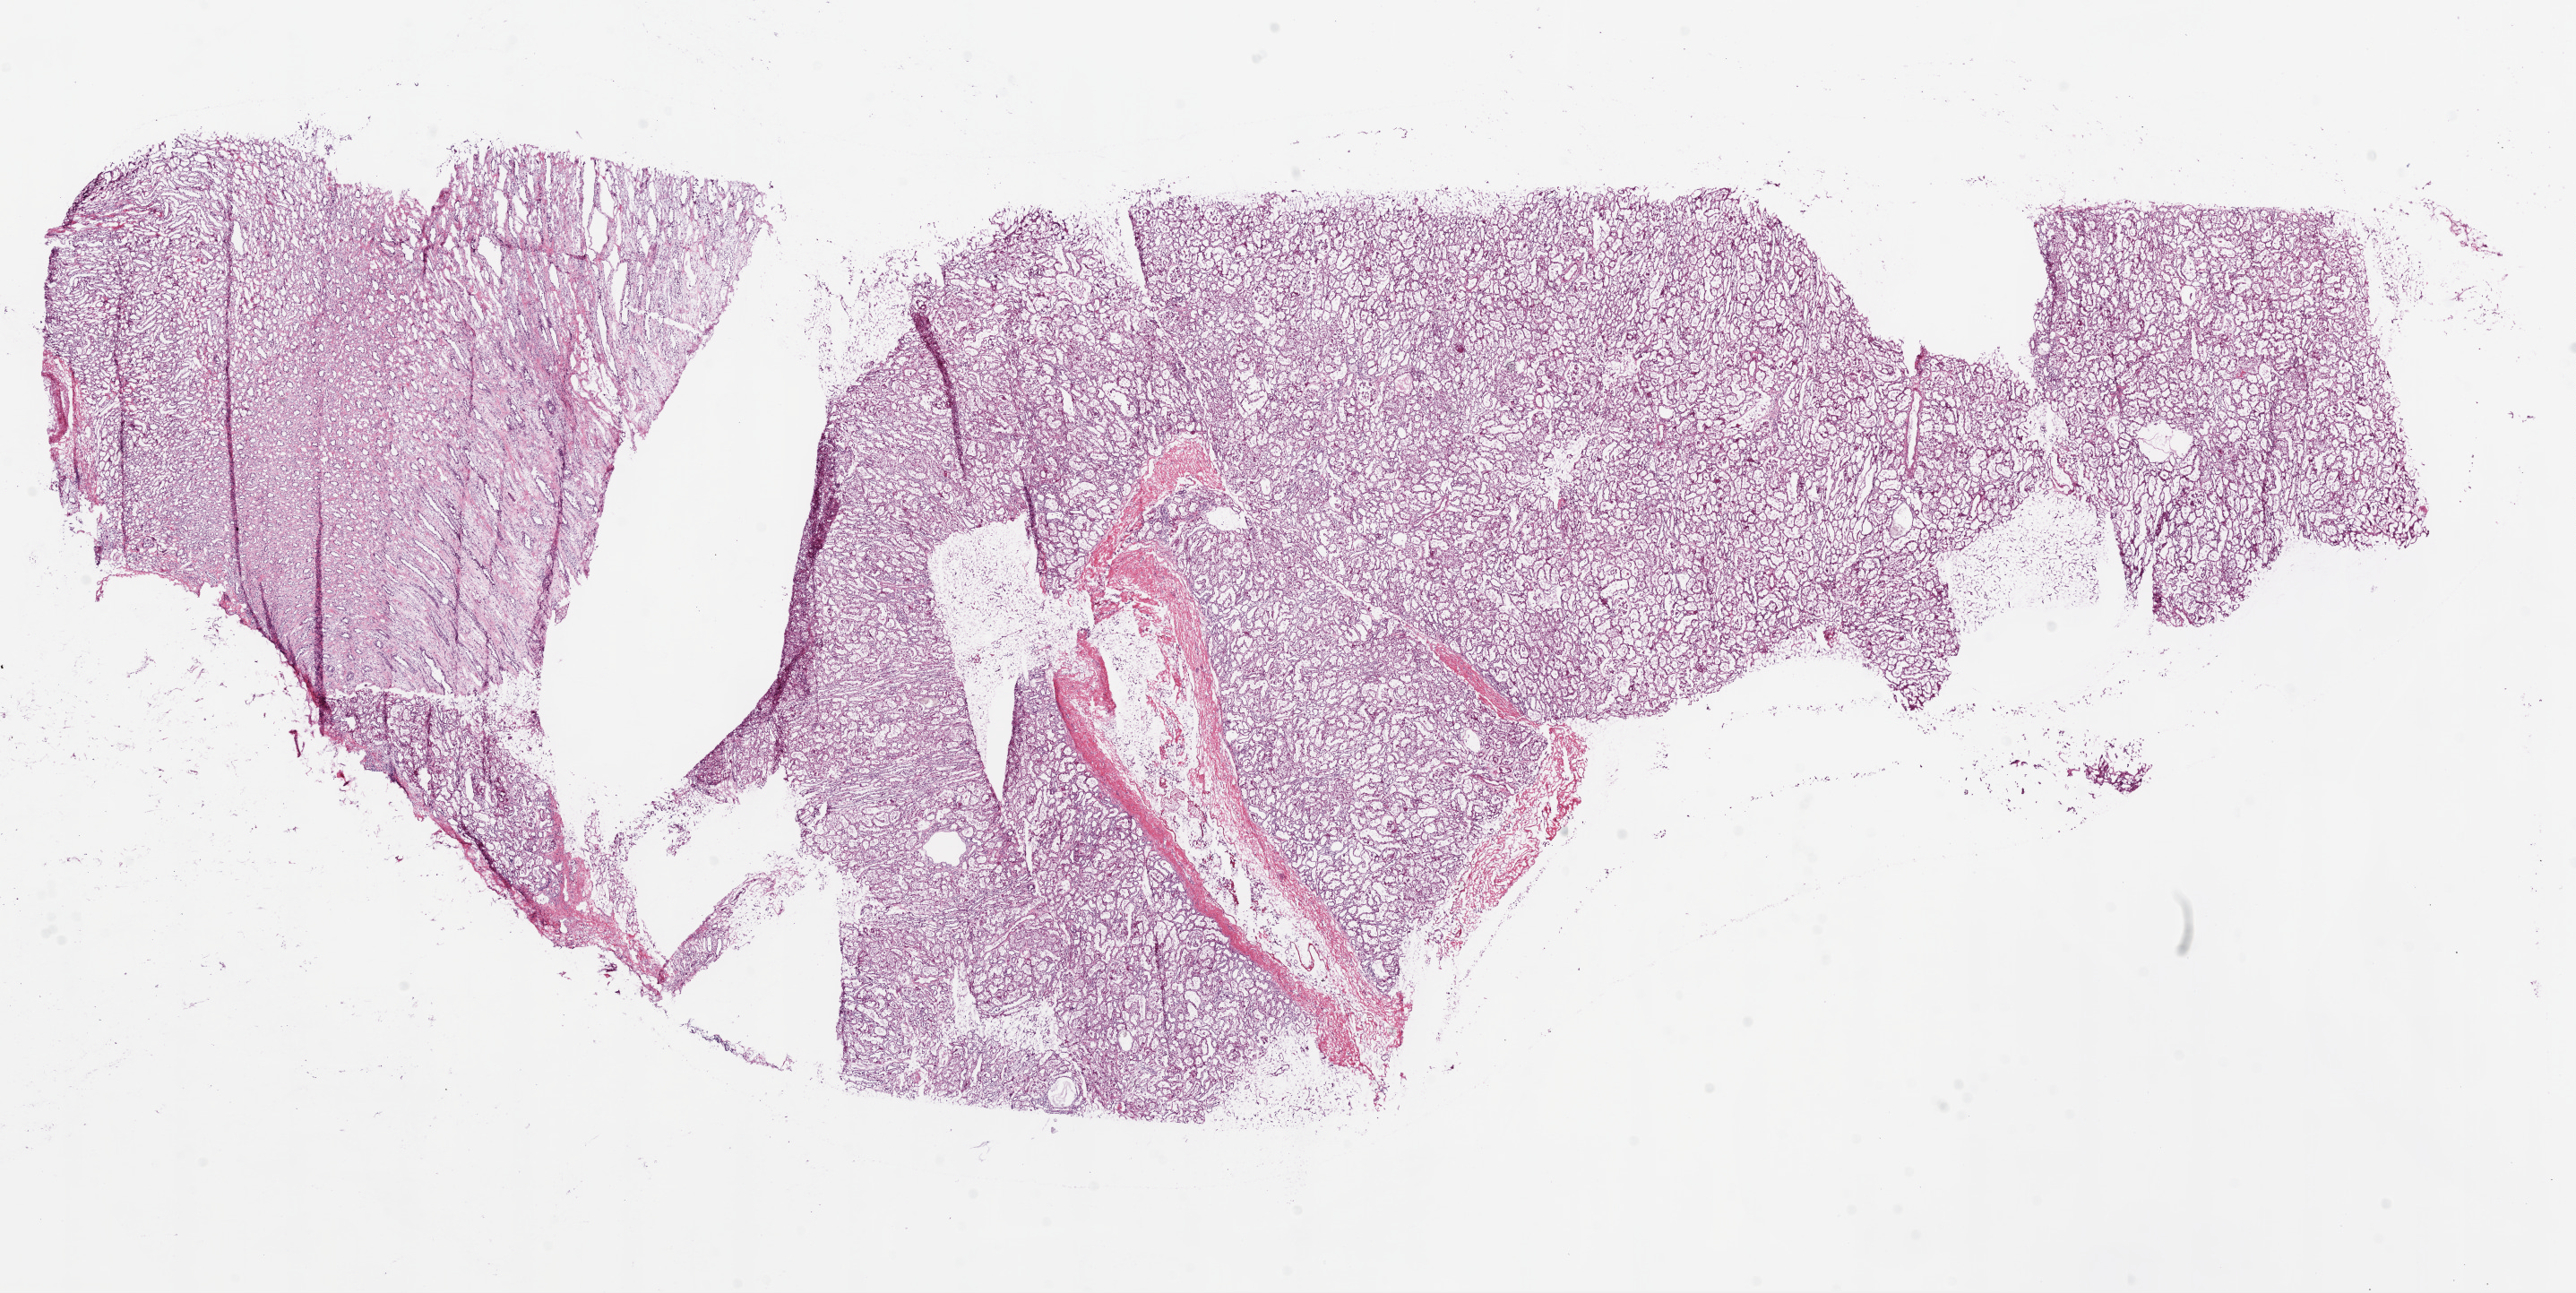
H&E whole-slide image, whole scanned area (about 23.1 x 11.6 mm, from a 20x scan) shown as a low-resolution overview; frozen section from the bottom of the tissue portion; sample: solid tissue normal (non-tumour tissue), kidney. Patient: female, age at initial diagnosis 48 years.
This section: solid tissue normal (non-tumour) sample from the same patient. Patient diagnosis: Clear cell adenocarcinoma, NOS.